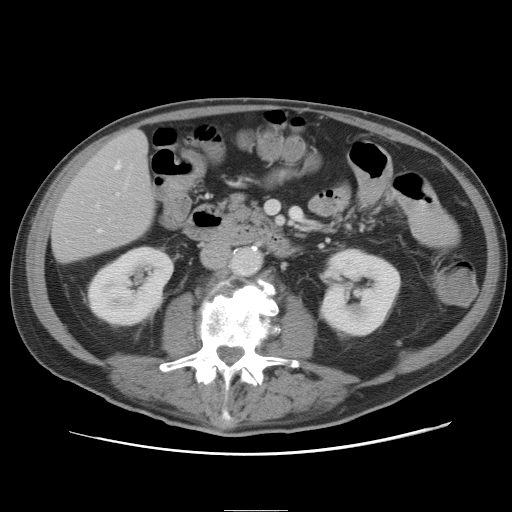
Contrast-enhanced abdominal CT, one axial slice. Slice 16 of 89 in the series (ordered by position). Intravenous contrast given. Soft-tissue window (W 400 / L 40 HU). 5 mm slice thickness. 512 × 512 image matrix, field of view 375 × 375 mm. Male patient, age 69 years. From the clinical record (not read from this slice): diagnosis: colorectal cancer liver metastases, imaged before liver resection; multiple liver metastases: no; largest metastasis: 8.5 cm.
Outlined on this slice (expert manual segmentation):
- hepatic veins: bounding box <99,161,121,232> (left, top, right, bottom; pixels)
- liver: <52,130,155,264>
- planned liver remnant (the part of the liver to remain after resection): <53,129,155,263>